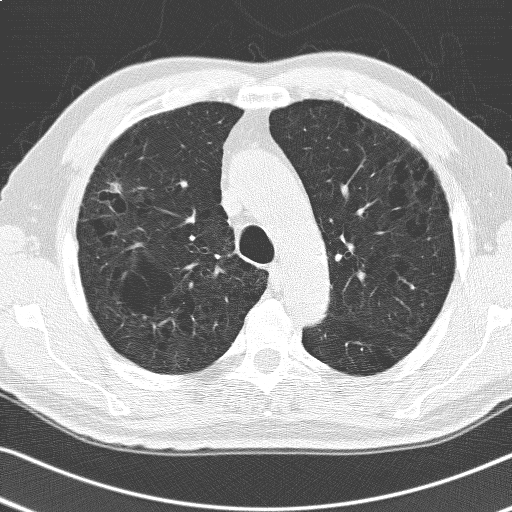
Low-dose screening chest CT, one axial slice; position 126 of 168 along the scan axis; 120 kVp; lung window (W 1500 / L -600 HU); 512 × 512 image matrix, field of view 336 × 336 mm.
Annotated regions visible in this slice (outlined manually by an expert reader):
- lesion 1 (tumor, upper lobe of right lung): box from (x=110, y=183) to (x=121, y=193) px